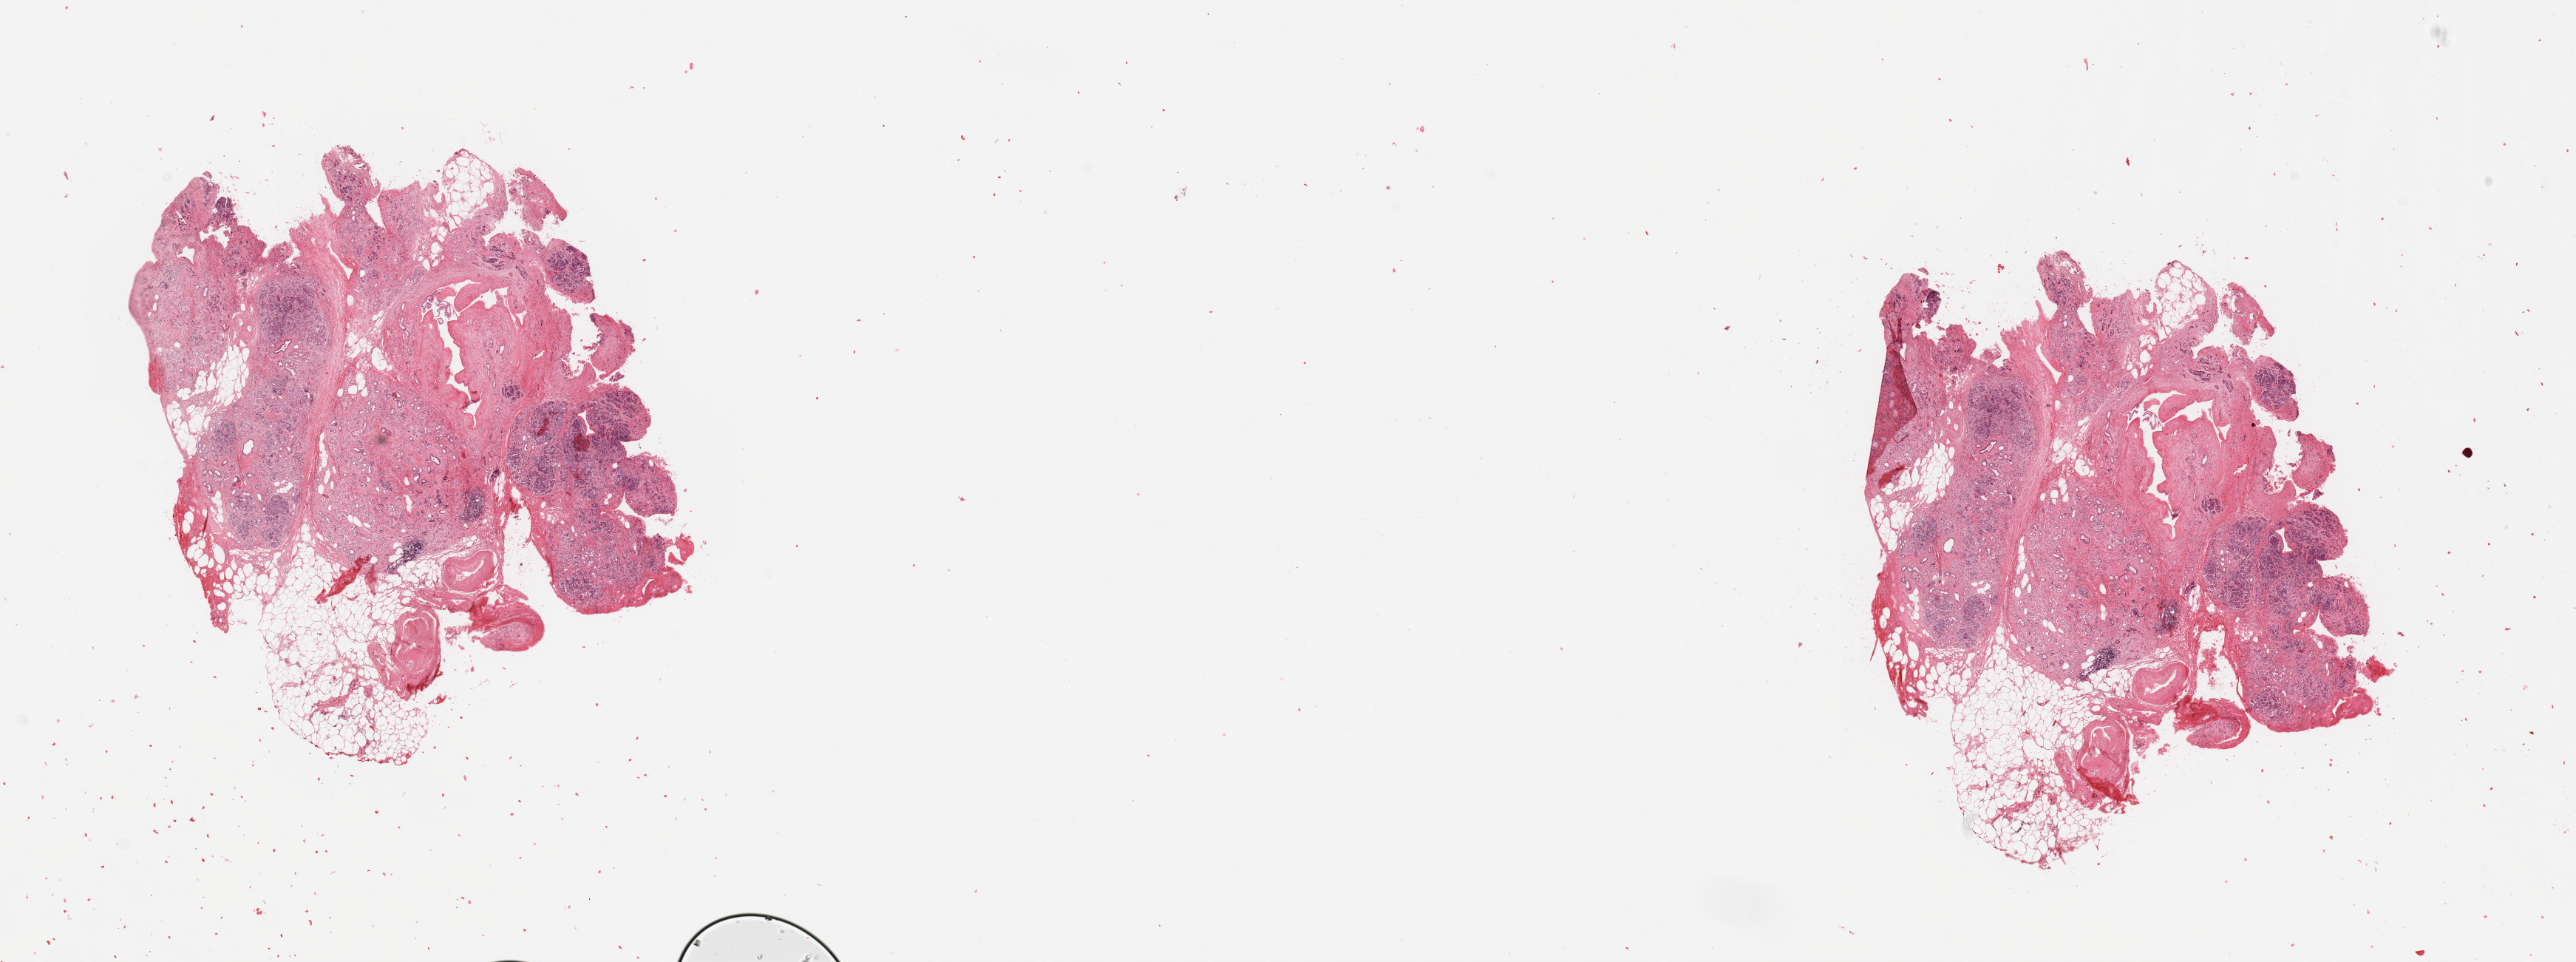
H&E-stained whole-slide image, shown as a low-resolution overview of the whole scanned area (about 27.6 x 10.3 mm, slide scanned at 20x). Normal (non-tumour) tissue sample, sampled site: pancreas. Patient: female, age 77 years.
This section: normal (non-tumour) tissue from the same patient. Patient diagnosis: Infiltrating duct carcinoma, NOS.